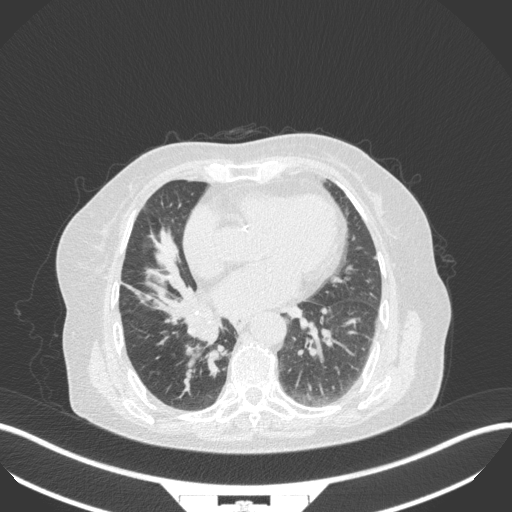
Chest CT, one axial slice. Slice 130 of 329 in the series (ordered by position). Lung window (W 1500 / L -600 HU). 1 mm slice thickness. 512 × 512 image matrix, field of view 400 × 400 mm. Patient: female, 75 years. From the clinical record (not read from this slice): clinical TNM (as recorded): T1b N0 M1a; histopathological grade: G1.
Structures marked on this image (bounding box drawn by a radiologist):
- lung tumour (recorded histology: squamous cell carcinoma): box from (x=179, y=310) to (x=227, y=348) px